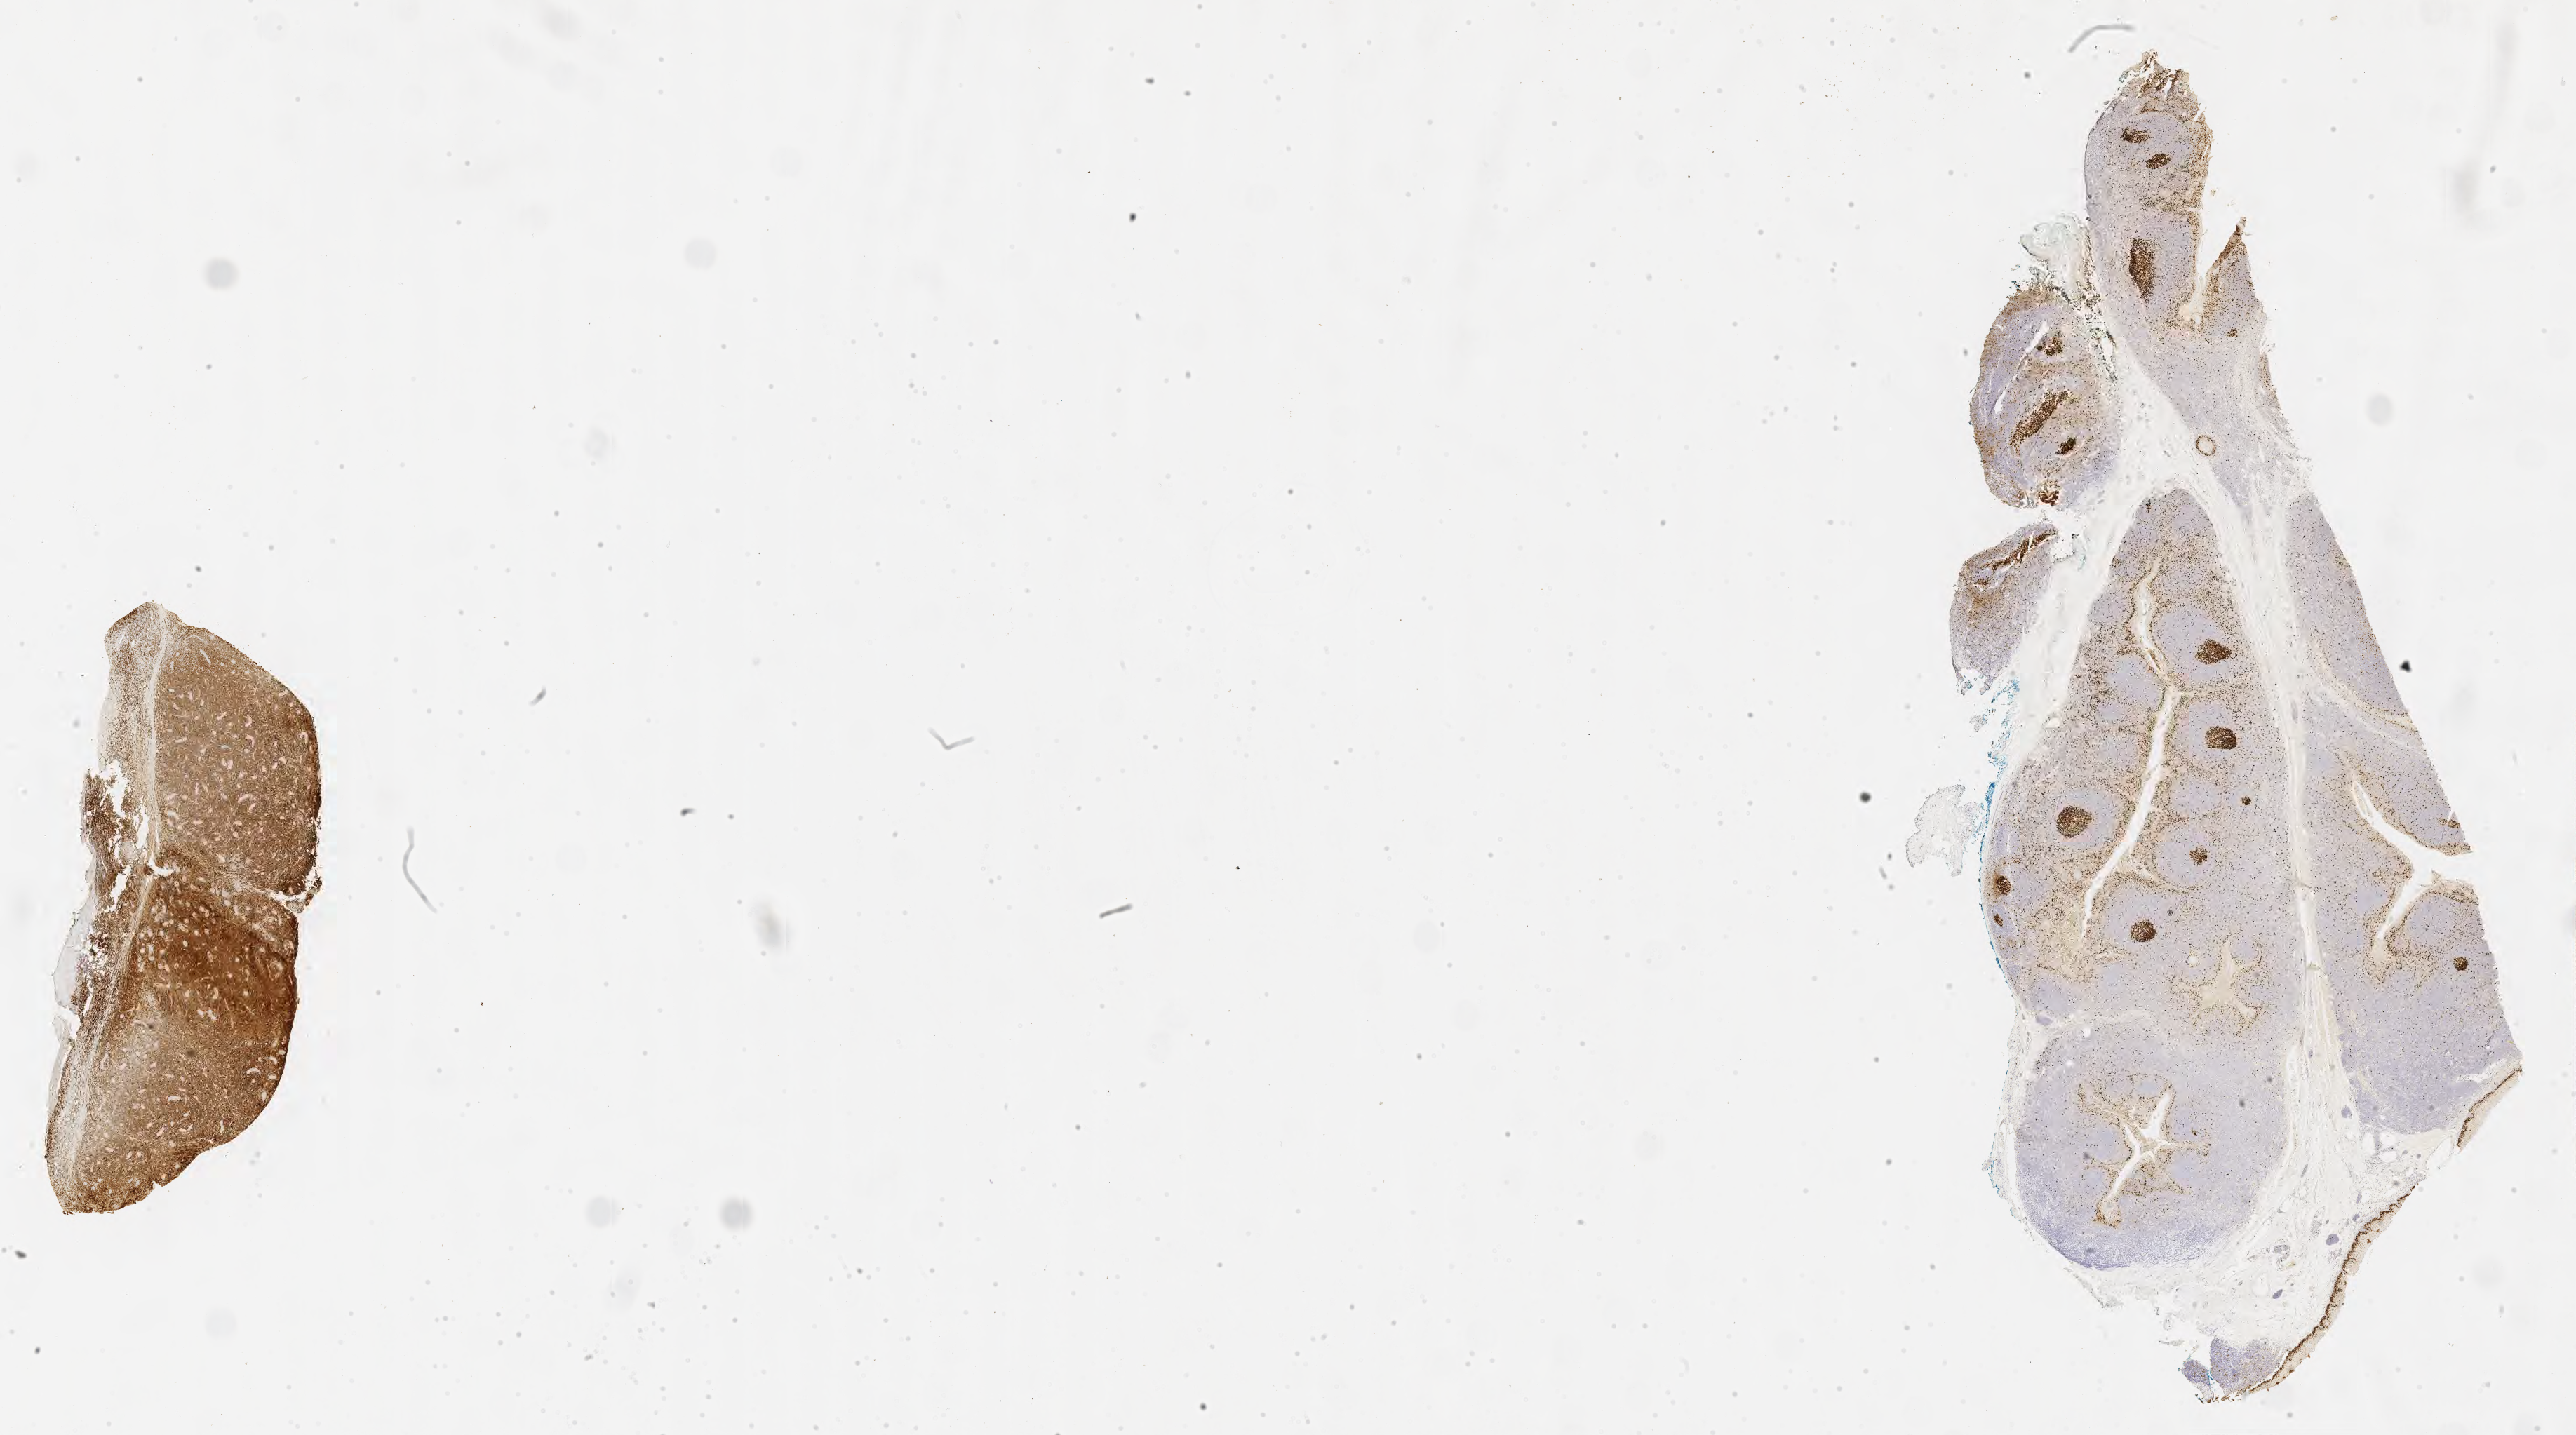
Immunohistochemistry (IHC) whole-slide image stained for Ki-67, a low-resolution overview of the entire scanned area, about 29.7 x 16.5 mm, specimen: tumor tissue, anatomic site: testis. Patient: male, age at initial diagnosis 8 years.
Diagnosis: Burkitt lymphoma, NOS.